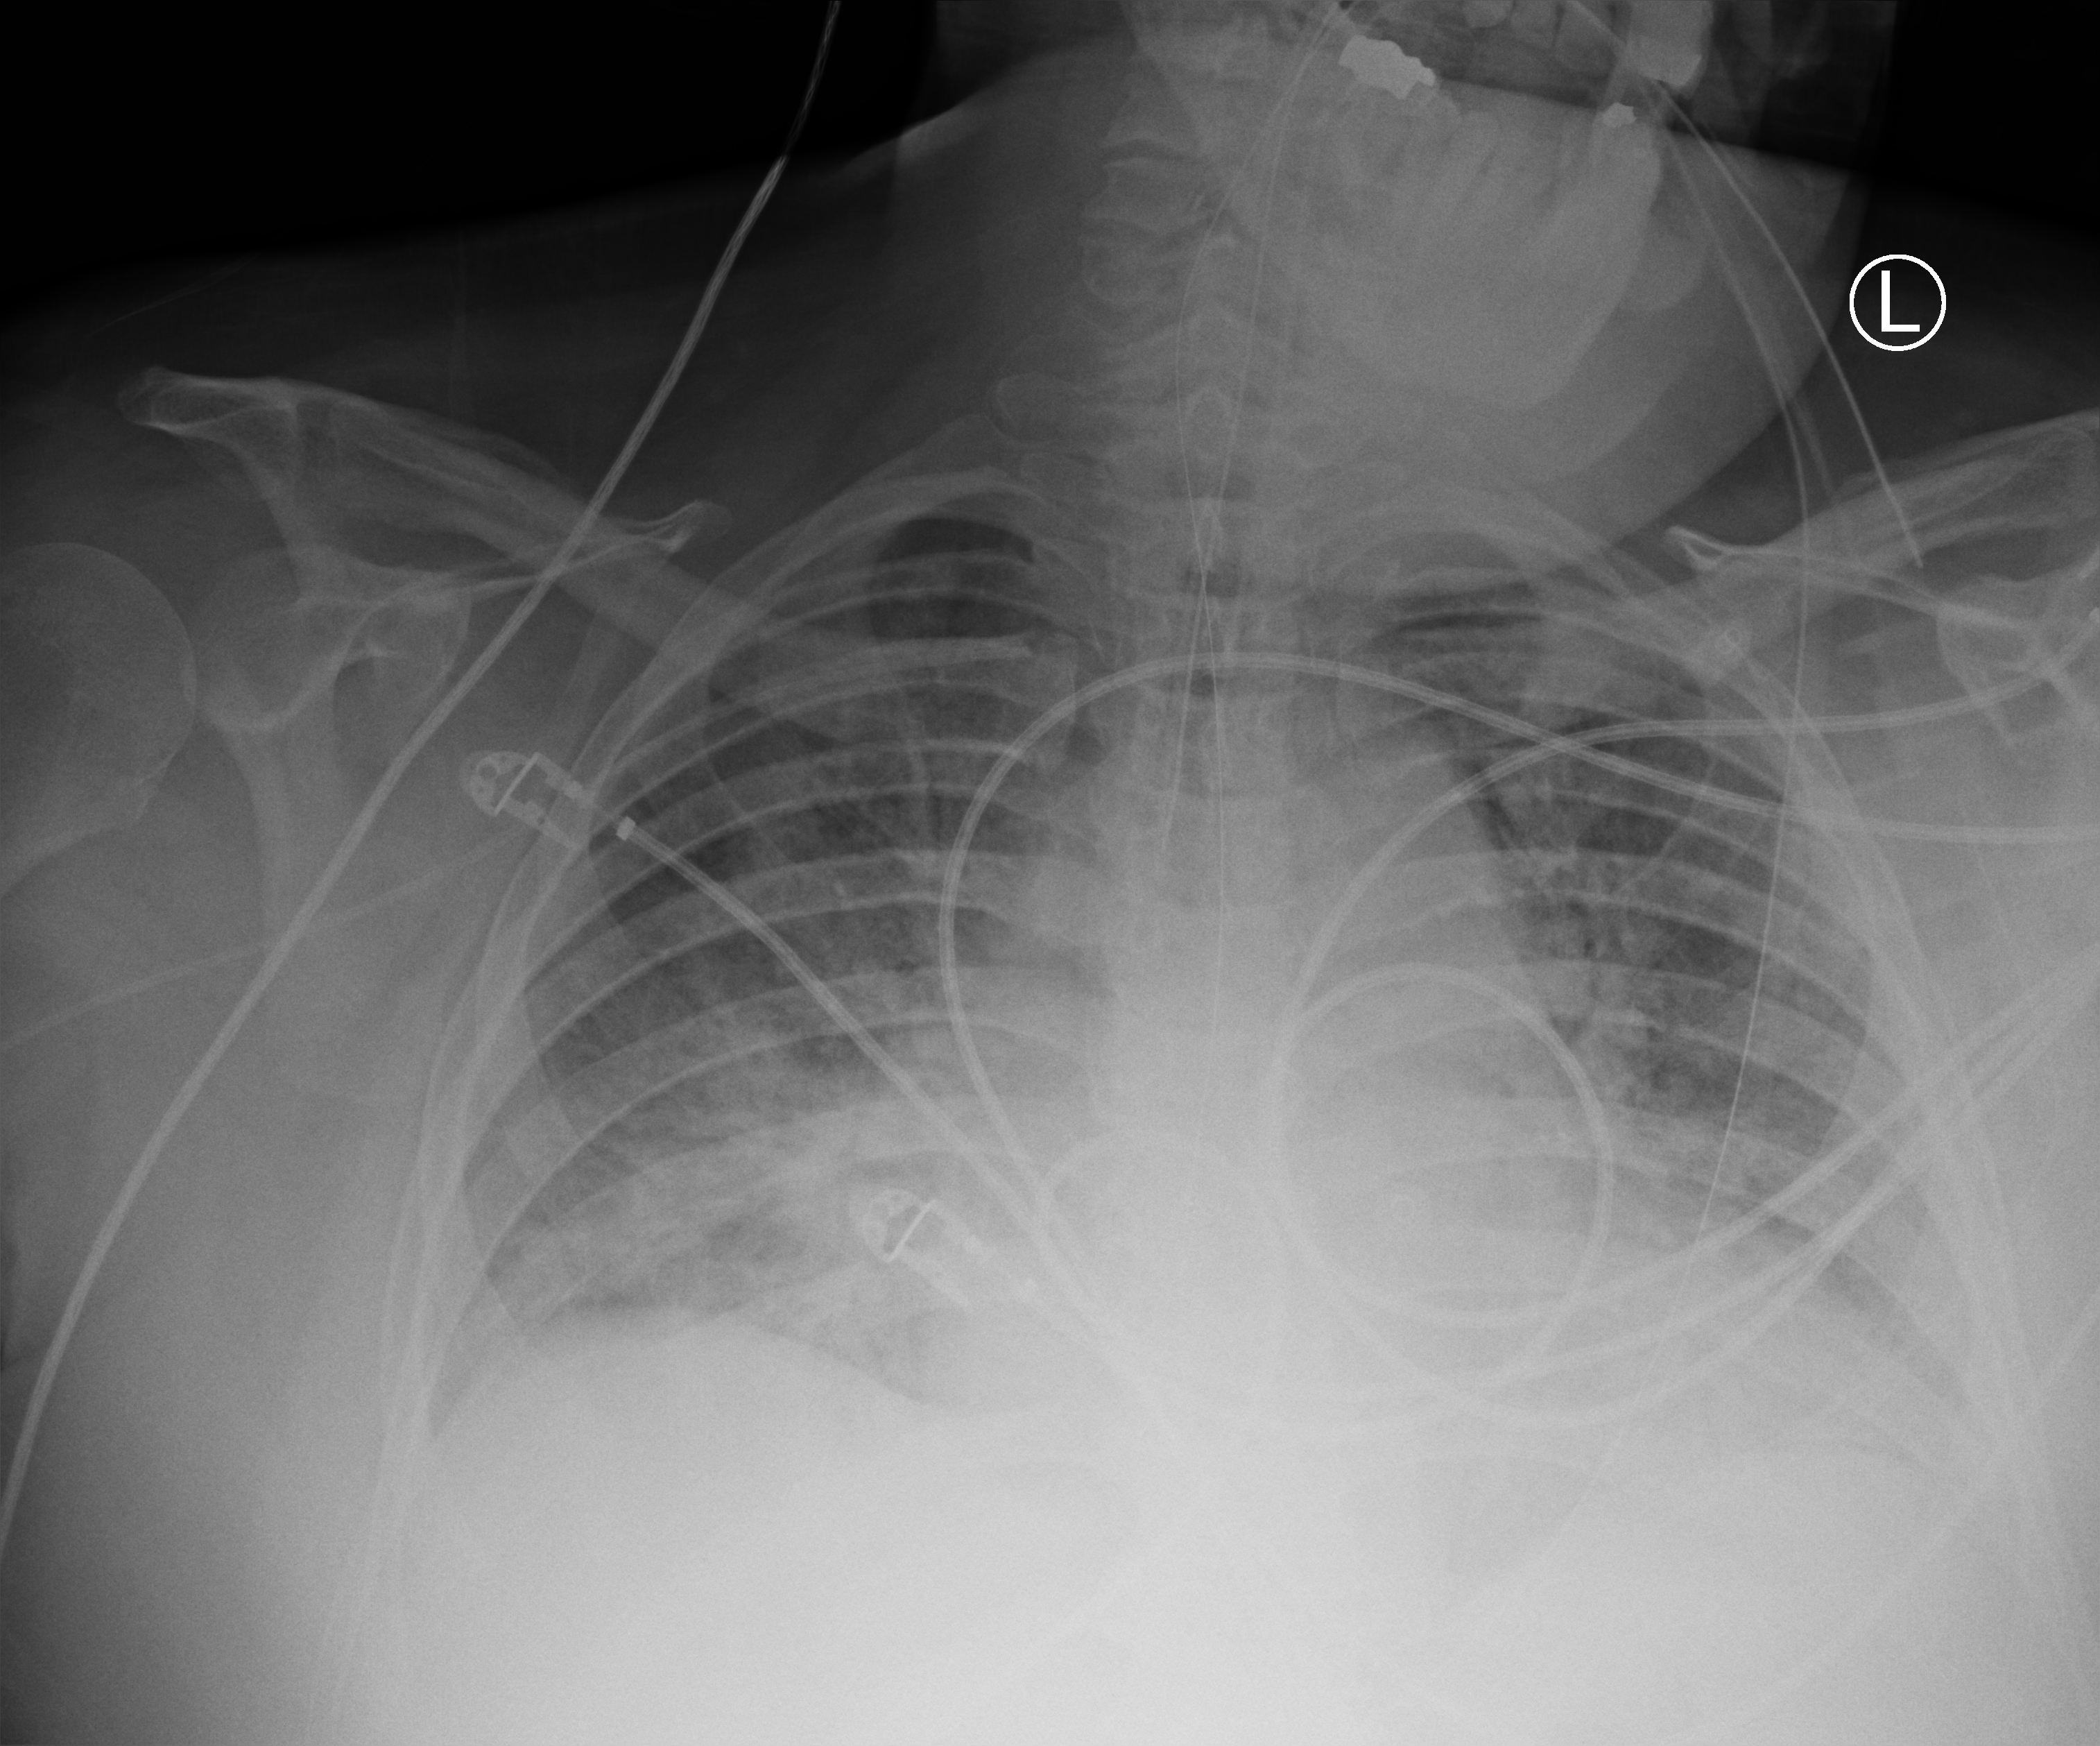
Portable chest radiograph, anteroposterior (AP) projection. Patient hospitalised with COVID-19; male, aged 18–59 years.
From the hospital-stay record, not from the radiograph (when in the stay this image was taken is not recorded): admitted to intensive care during this hospital stay: yes; smoking status (admission record): never.